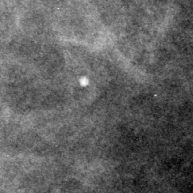
Crop from a digitized film mammogram around one marked abnormality; left breast; CC view; BI-RADS breast density category 2 (scale 1–4).
Calcifications, morphology punctate; BI-RADS assessment category 2; benign without callback (not worked up further).